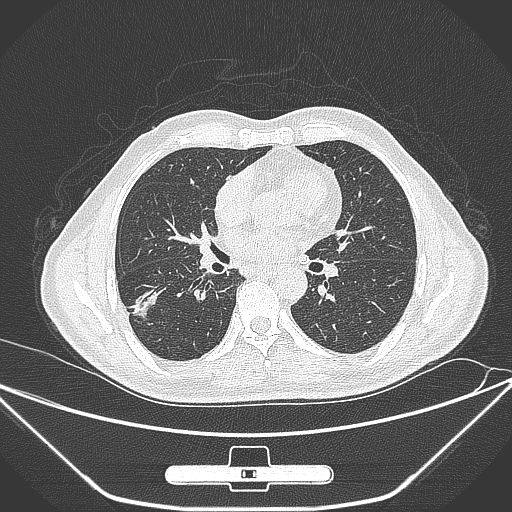
Chest CT, one axial slice; position 144 of 309 along the scan axis; 120 kVp; lung window (W 1500 / L -600 HU); 512 × 512 image matrix, field of view 398 × 398 mm. Male patient, age 71 years. From the clinical record (not read from this slice): clinical TNM (as recorded): T1c N0 M0; histopathological grade: G2.
Annotated regions visible in this slice (rectangle marked by the reading radiologist):
- lung tumour (recorded histology: adenocarcinoma): box from (x=126, y=274) to (x=167, y=327) px